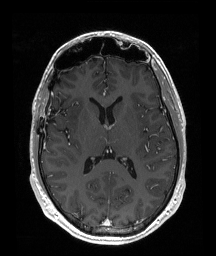
Brain MRI from a brain-tumour surgery series, one axial slice; slice 97 of 192 in the series (ordered by position); T1-weighted post-contrast; 1 mm slice thickness; 216 × 256 image matrix, field of view 219 × 260 mm. From the clinical record (not read from this slice): histopathology: Astrocytoma; WHO grade: 2; IDH mutation: yes.
Structures marked on this image (expert manual segmentation):
- tumour: bounding box <67,108,81,127> (left, top, right, bottom; pixels)